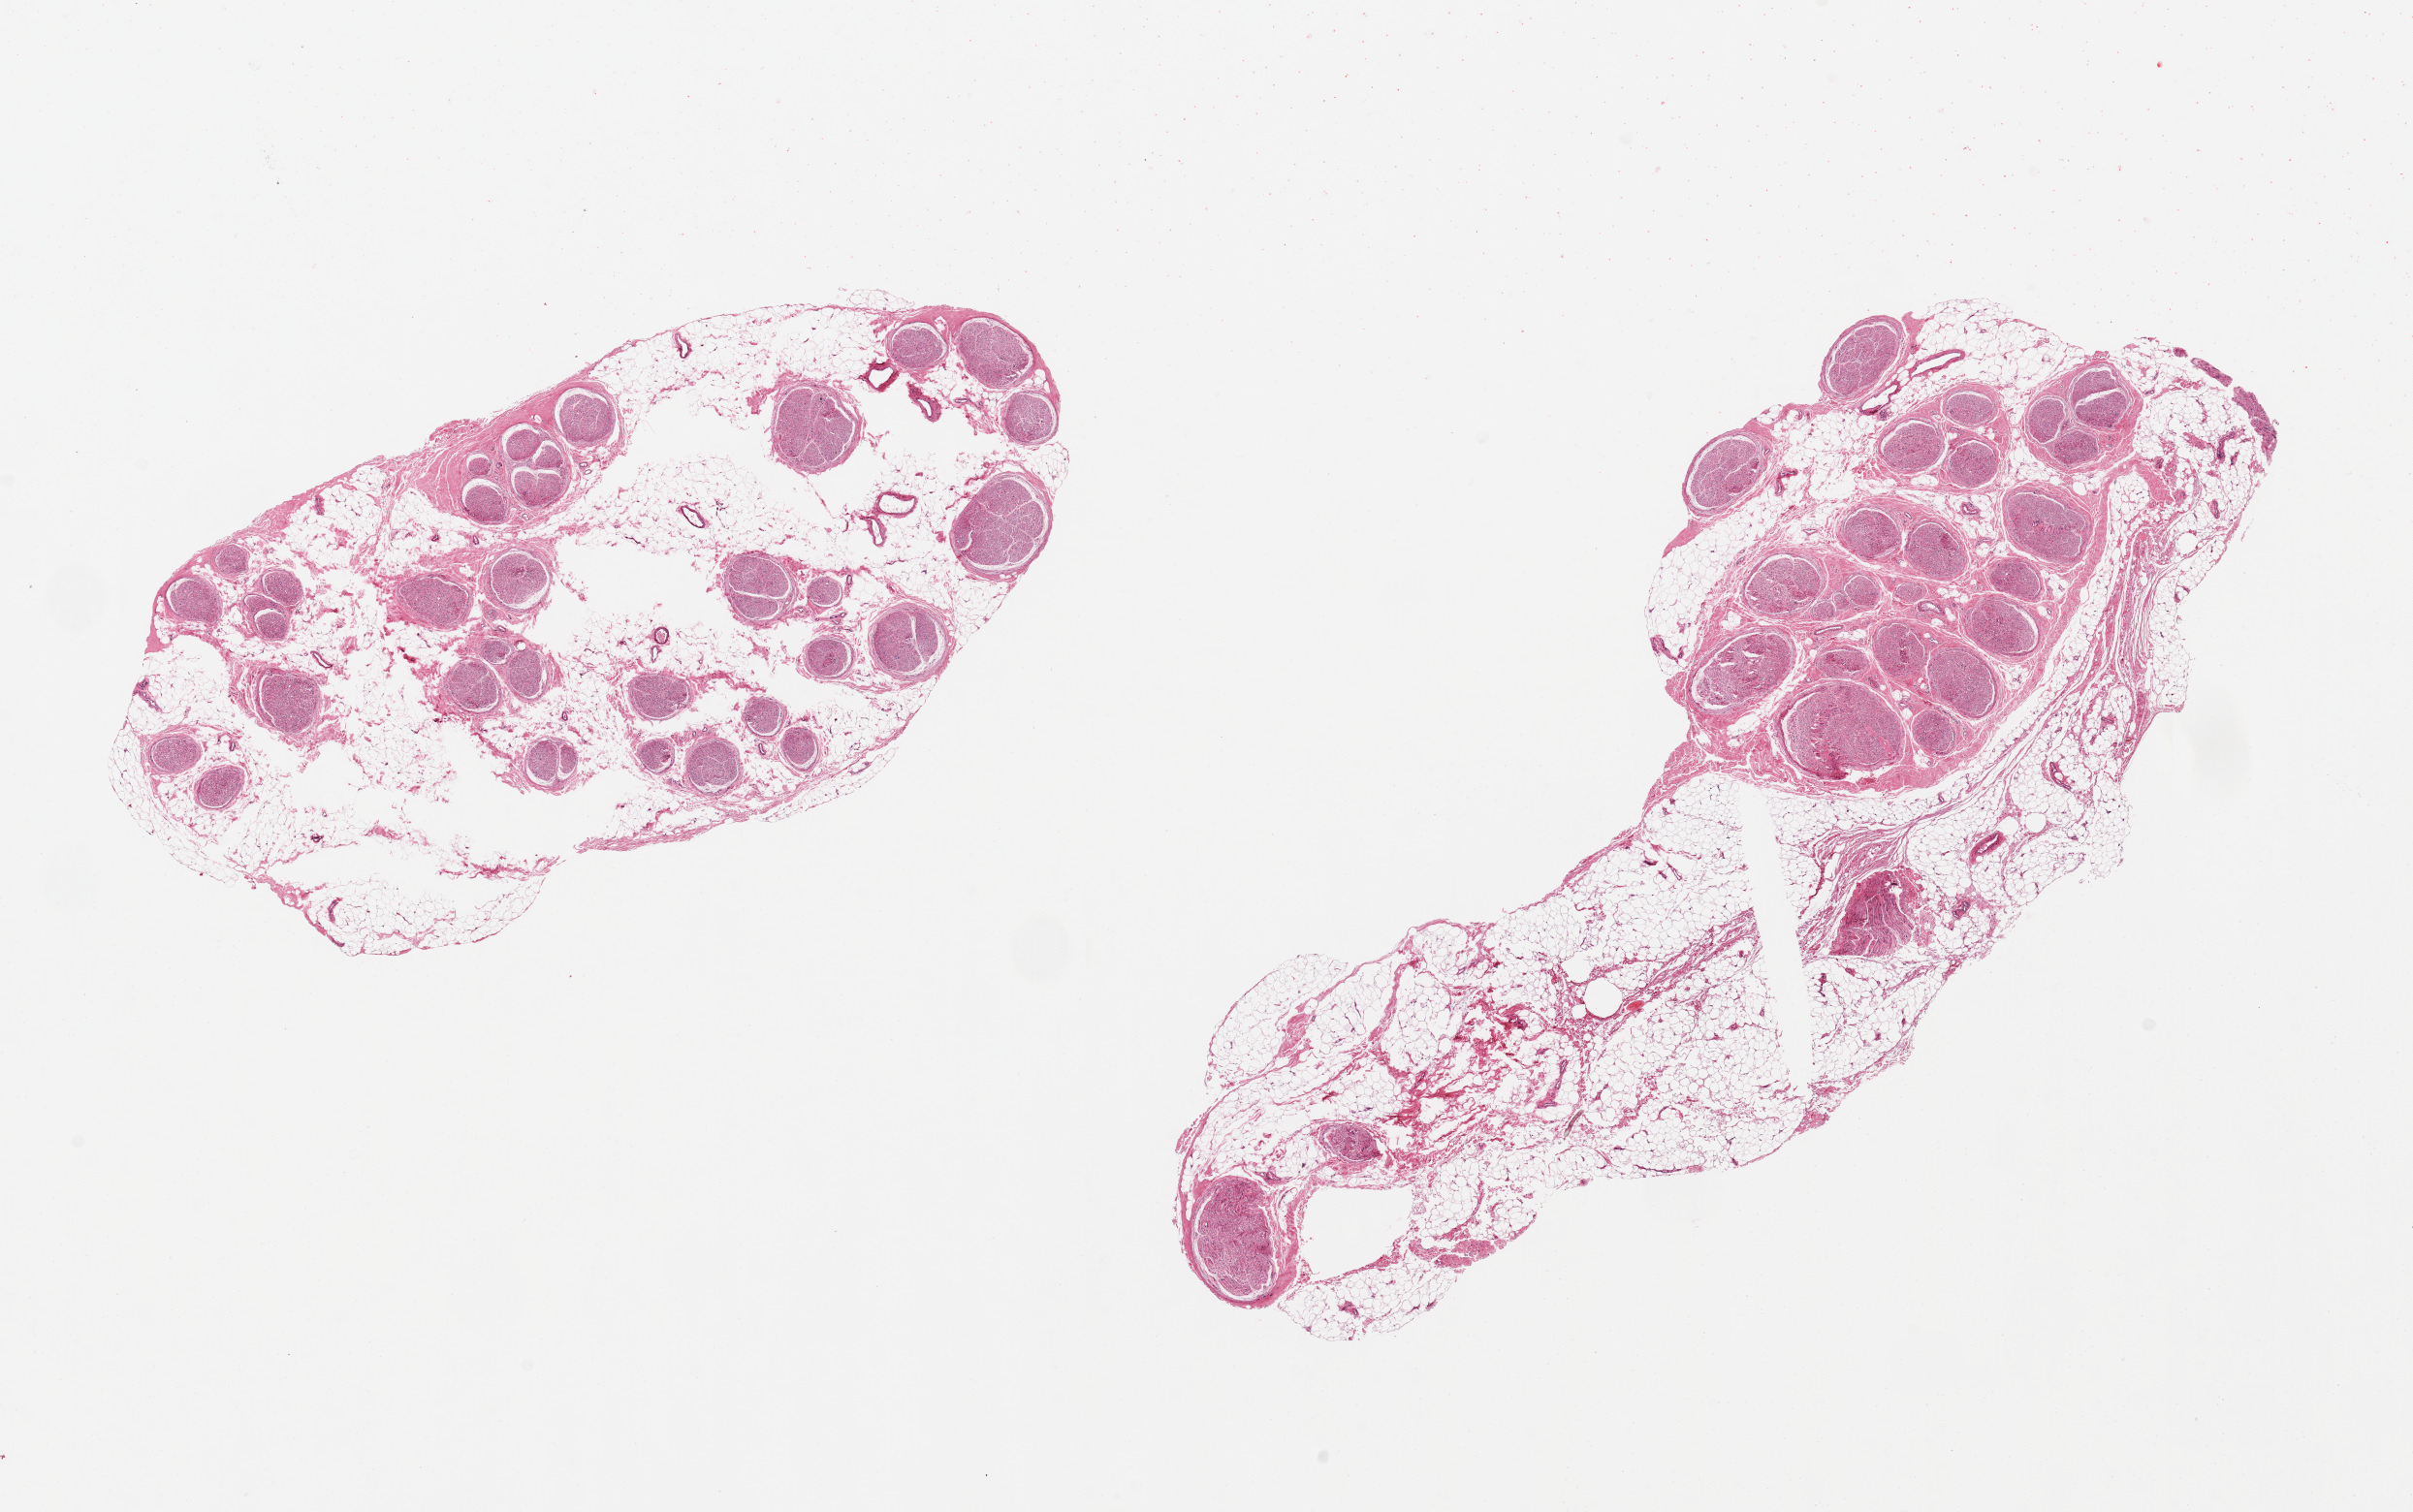
Whole-slide image, H&E stain, whole scanned area (about 19.7 x 12.3 mm, acquisition: 20x scan) shown as a low-resolution overview. PAXgene-fixed, paraffin-embedded tissue. Section of tibial nerve (target tissue). Tissue donor sample. Male donor.
• review note (as recorded): 2 pieces 11x5&8x4 mm; 60% adipose